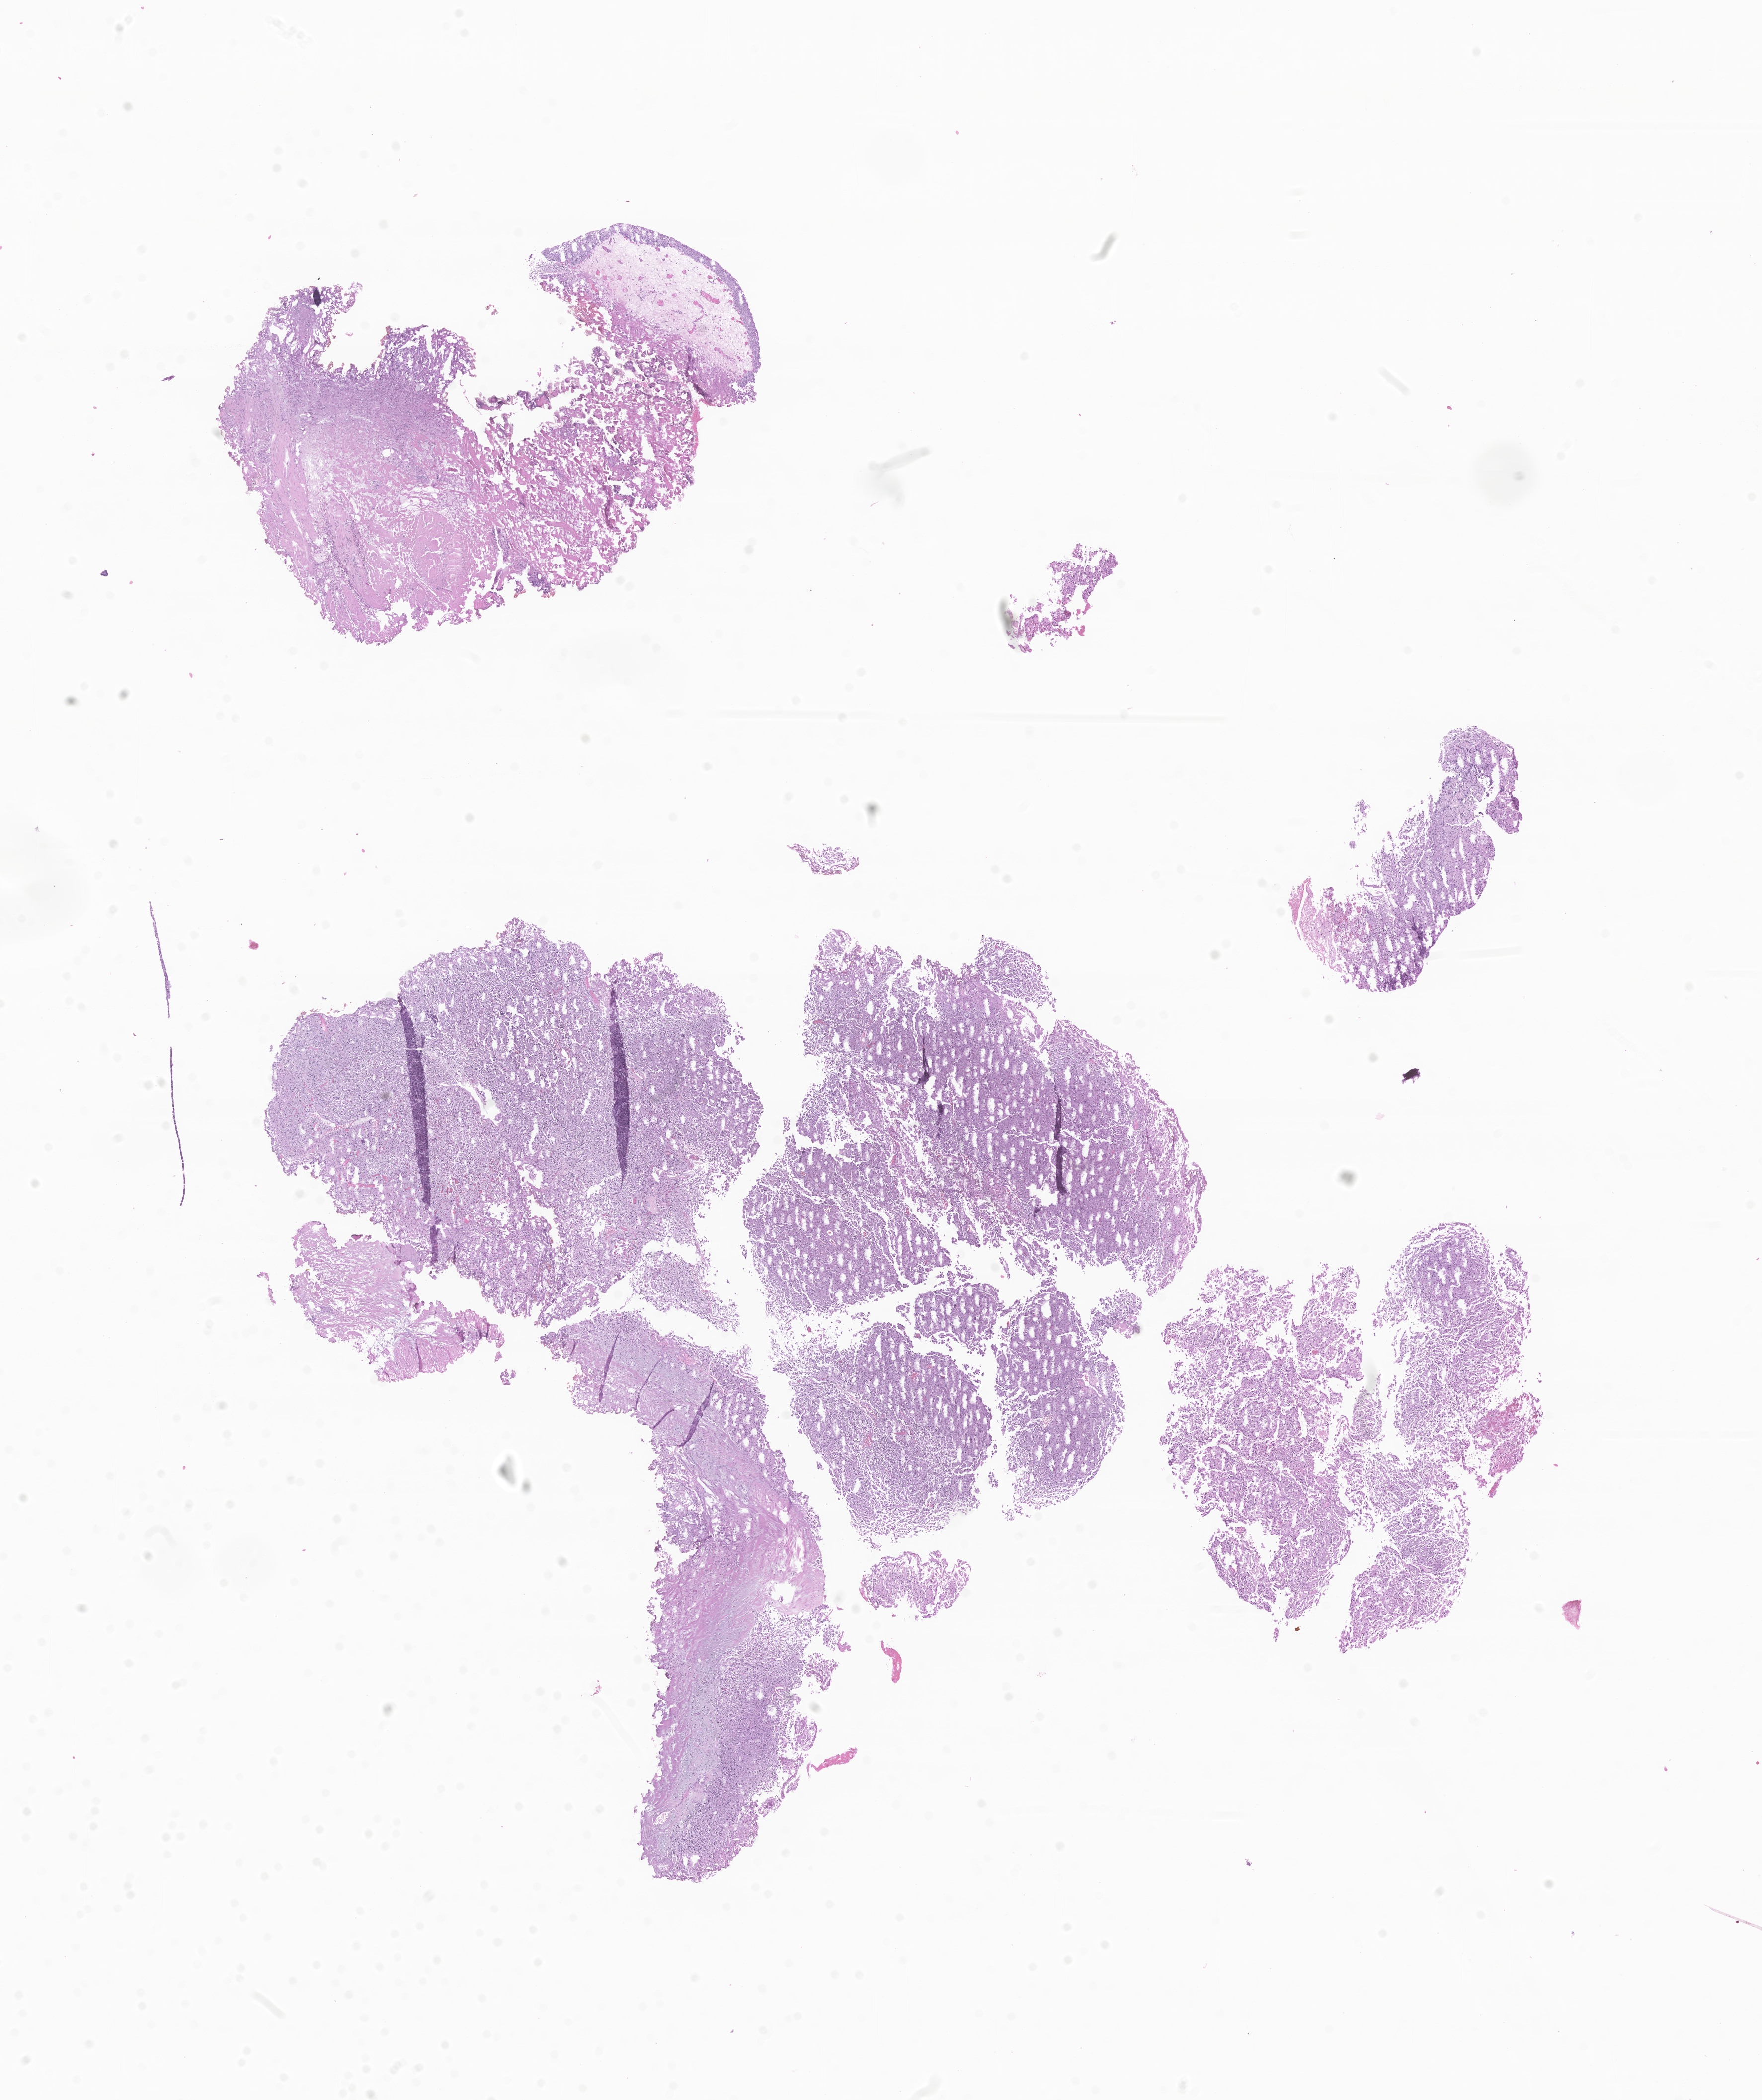
Whole-slide image, haematoxylin and eosin stain of tumor tissue from the urinary bladder, shown as a low-resolution overview of the whole scanned area (about 14.9 x 17.8 mm), formalin-fixed, paraffin-embedded (FFPE) tissue. Patient: female, age 174 months (14 years 6 months).
Recorded diagnosis: Neoplasm, uncertain whether benign or malignant.